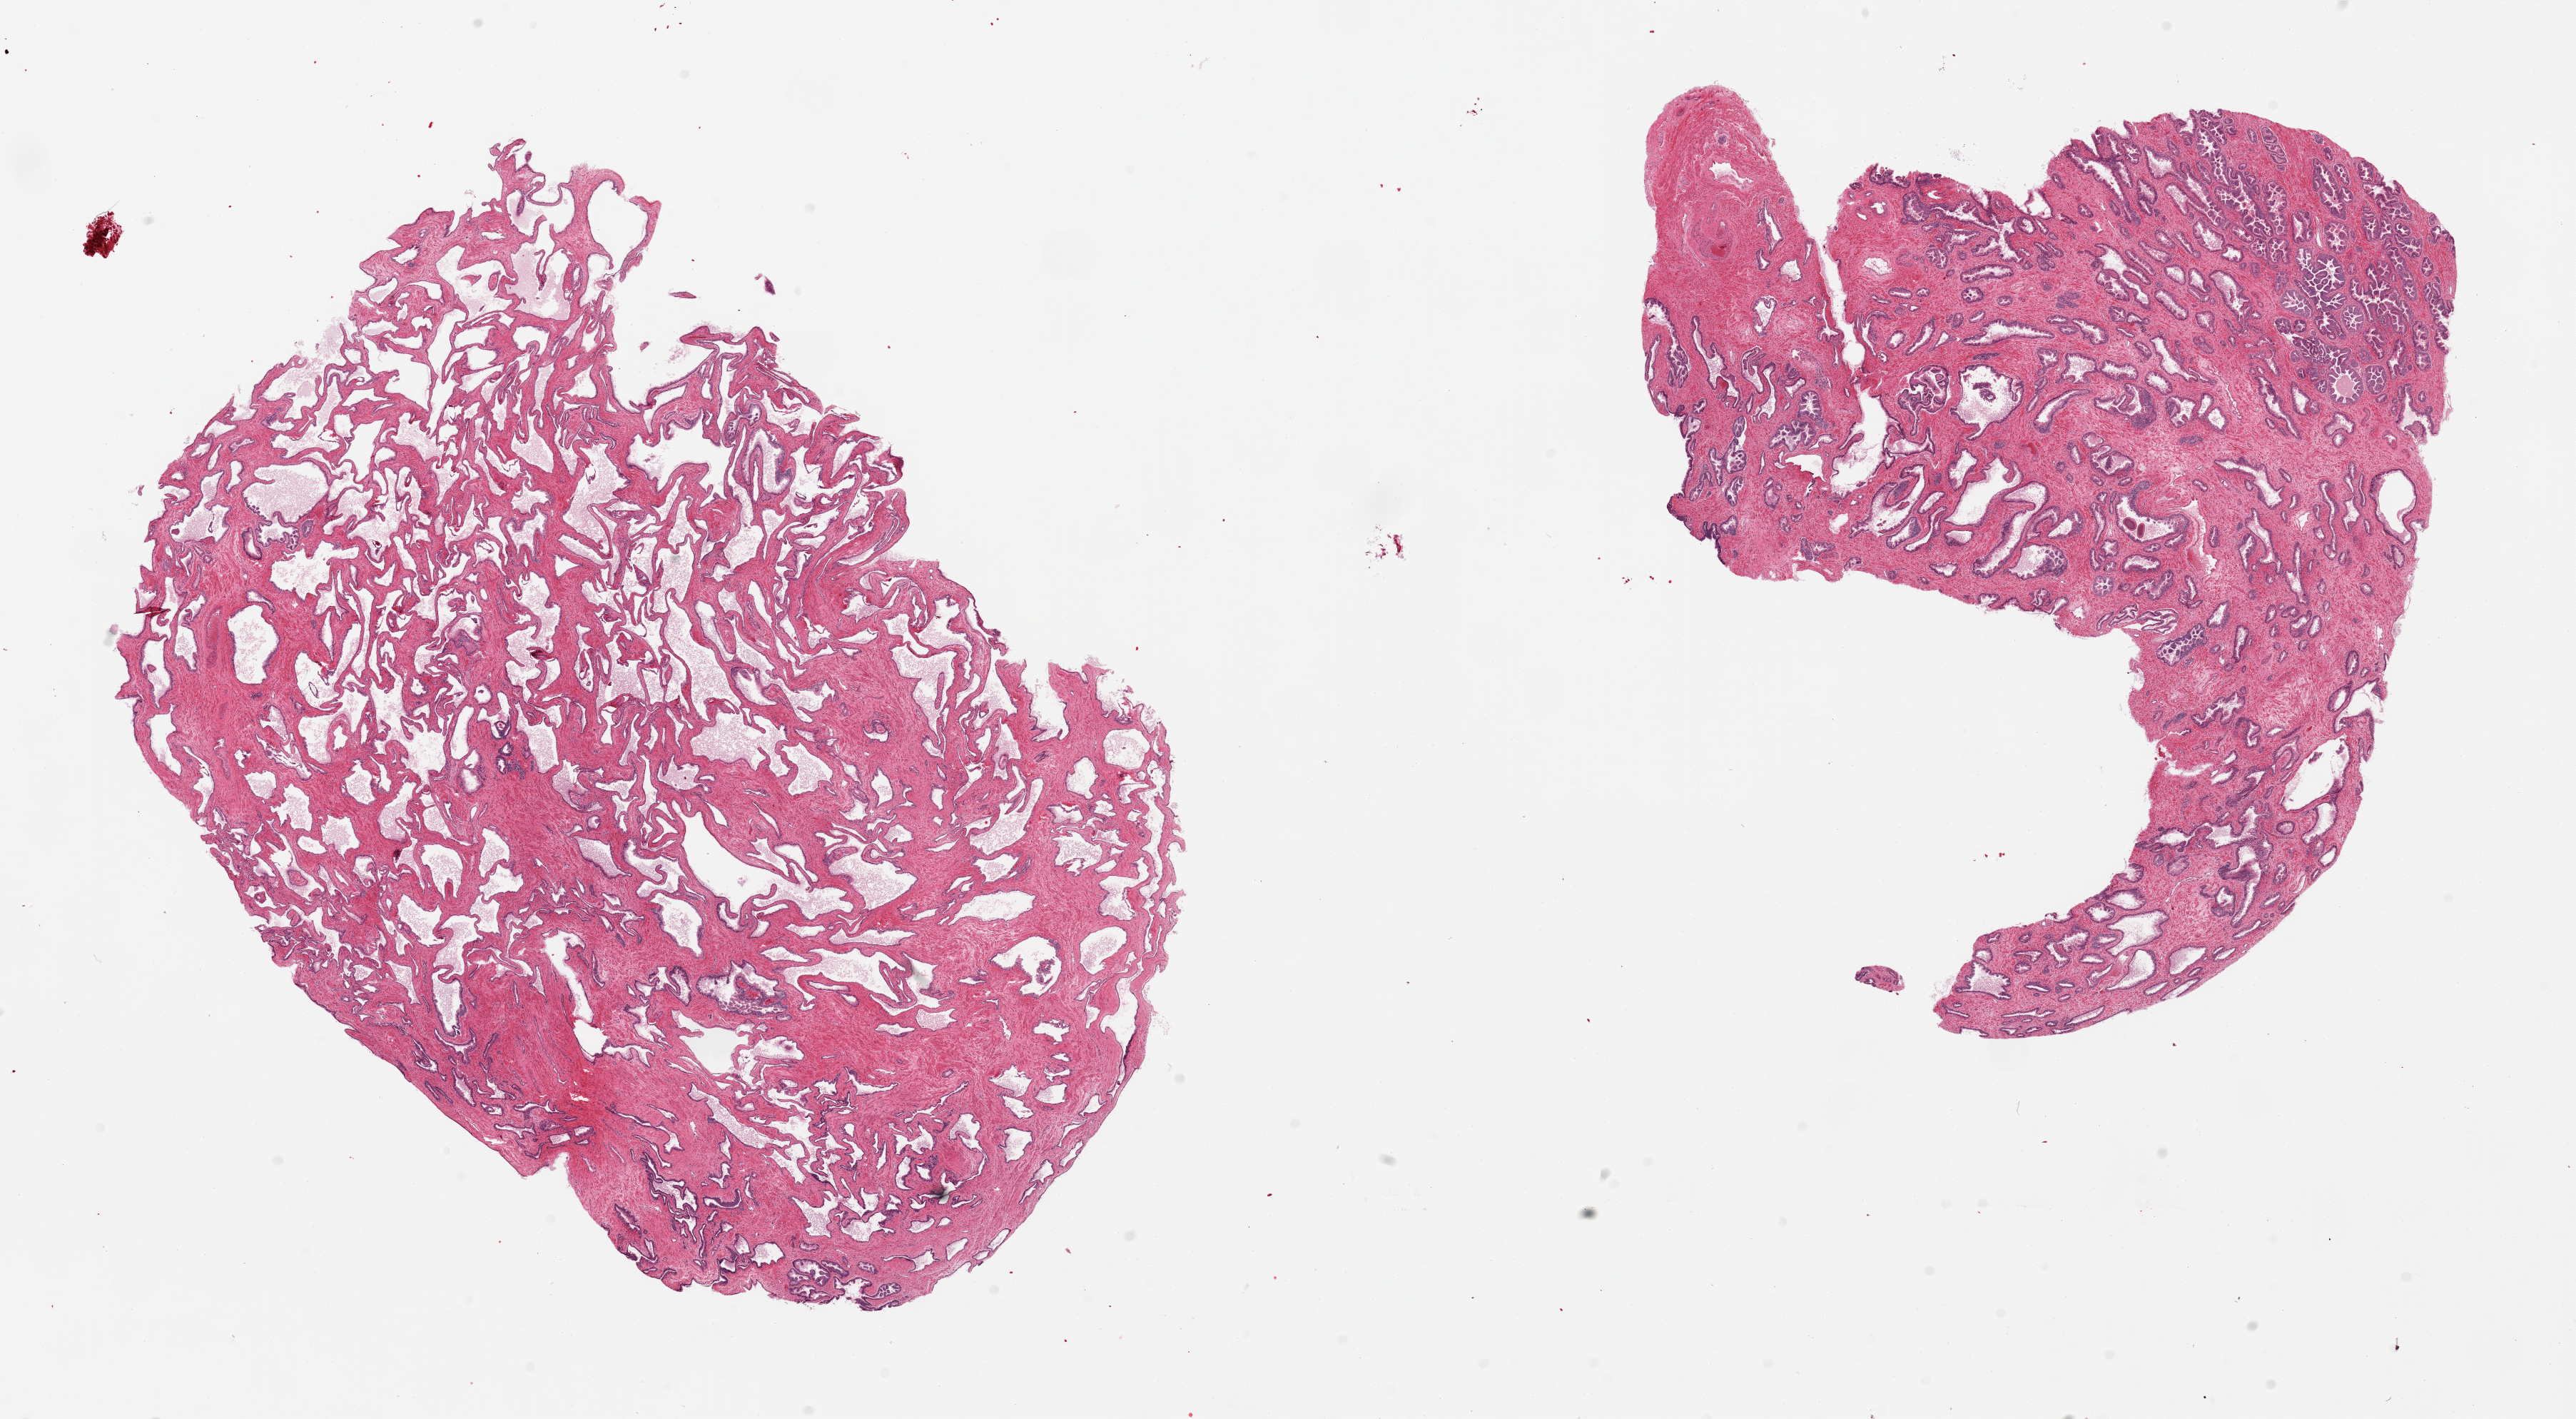
H&E whole-slide image — a low-resolution overview of the entire scanned area, about 28.5 x 15.7 mm (acquisition: 20x scan). PAXgene-fixed paraffin-embedded (PFPE) section. Sampled site (target tissue): prostate. Tissue donor sample.
Pathologist's review note for this sample: 2 pieces, epithelium largely sloughed in one piece with dilated glands.